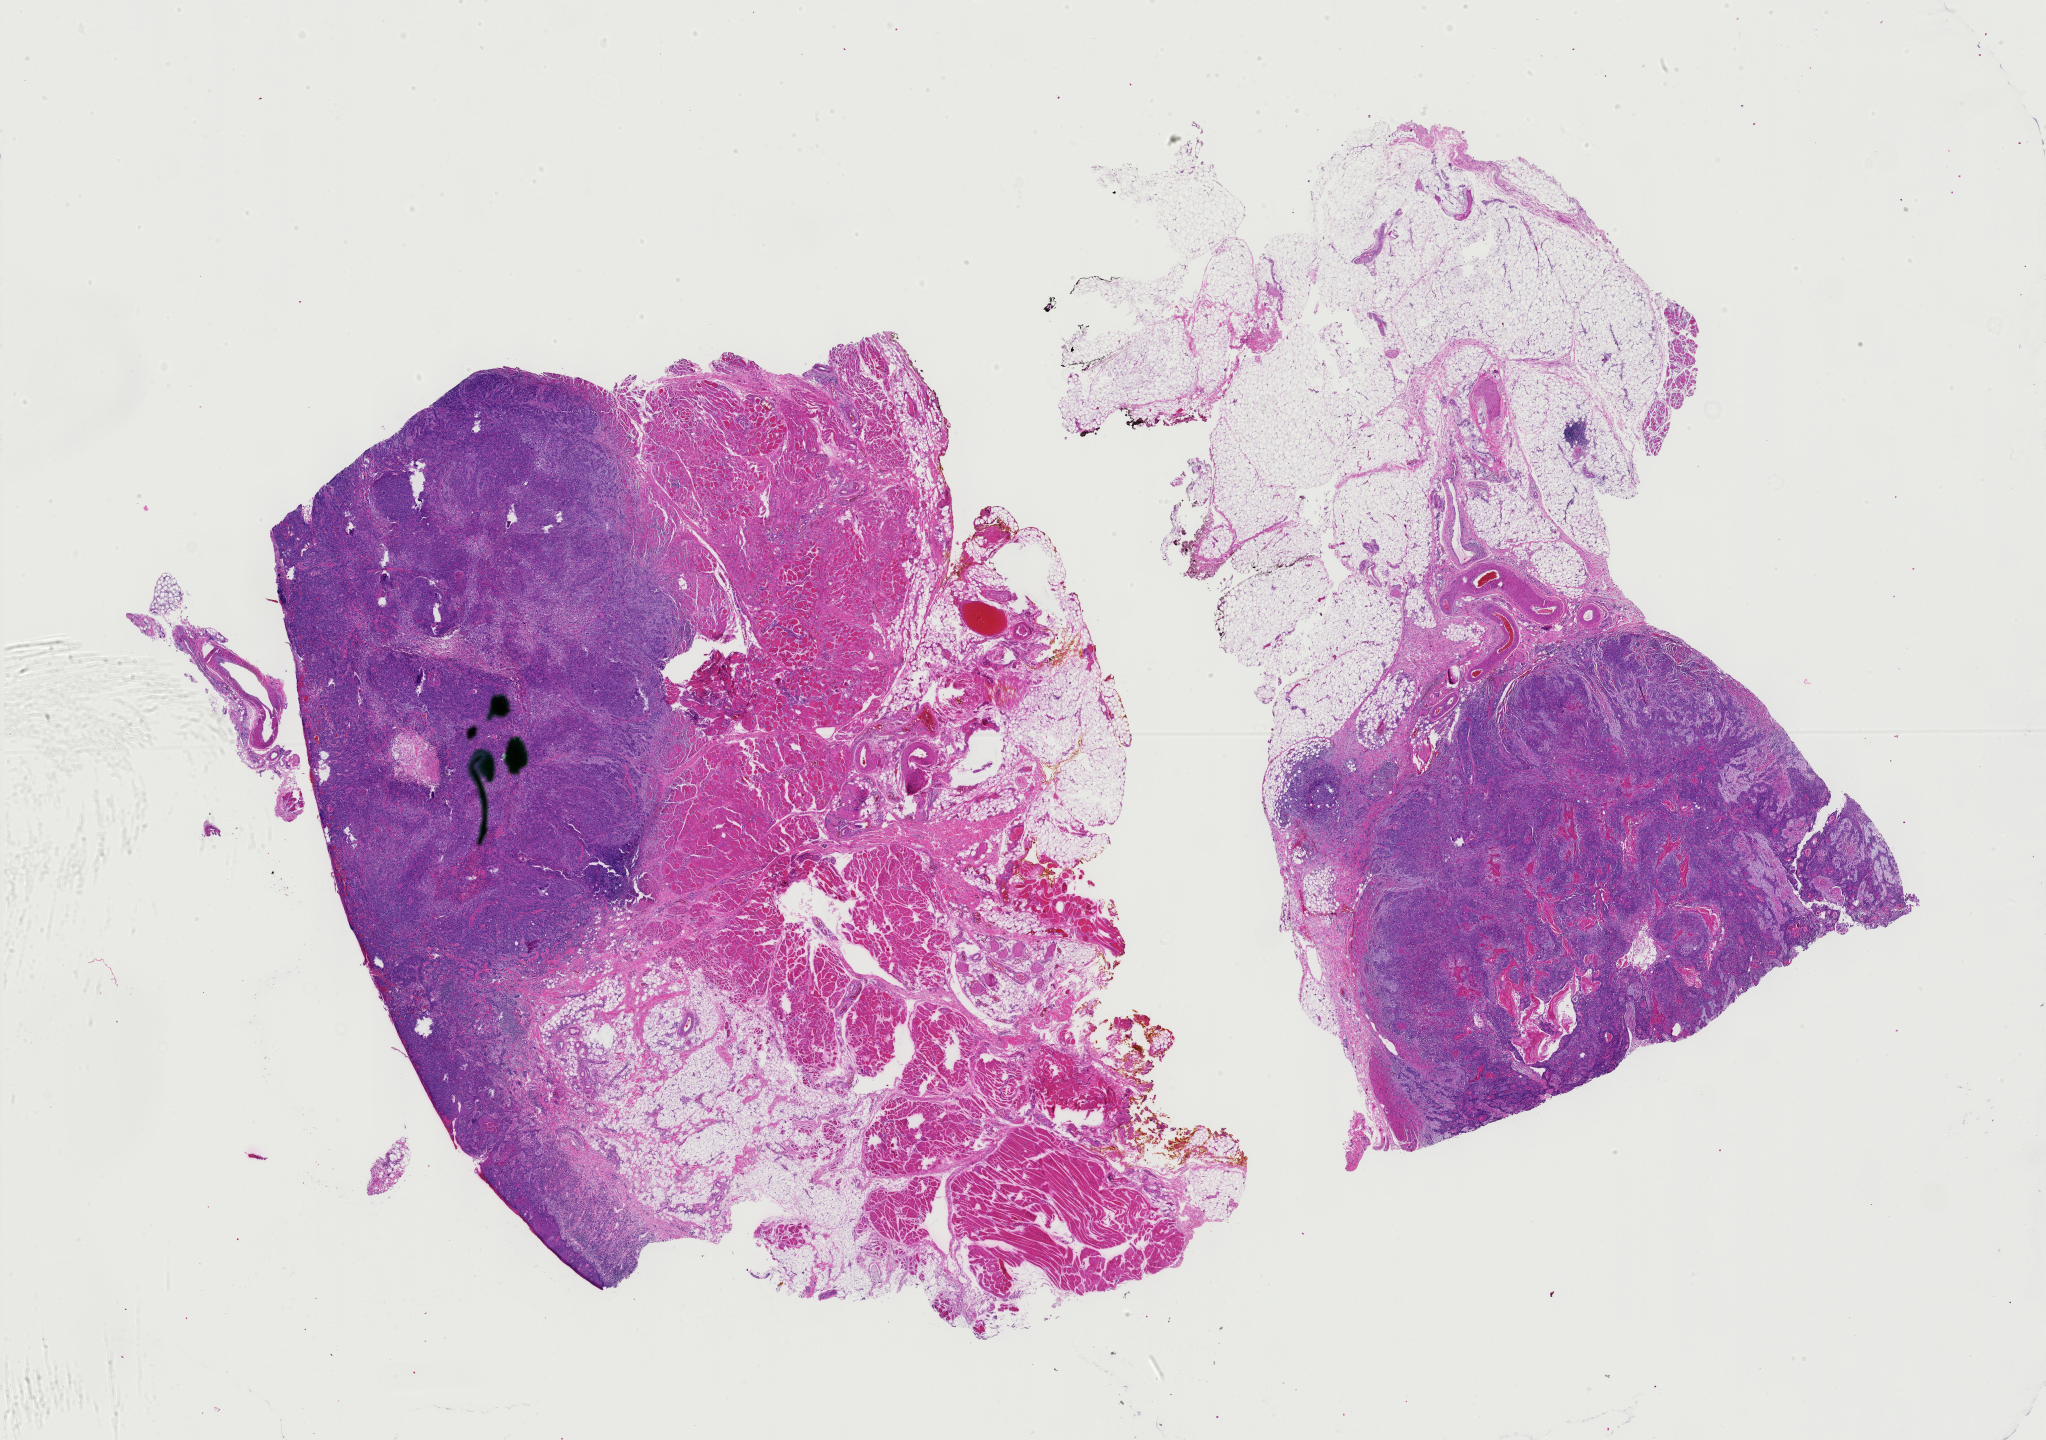
Whole-slide histology image, H&E-stained, whole scanned area (about 29.7 x 20.9 mm, slide scanned at 40x) shown as a low-resolution overview, formalin-fixed paraffin-embedded (FFPE) diagnostic section, primary tumour sample from the head and neck. Male patient; age at initial diagnosis 69 years. Histologic grade: G2 (moderately differentiated).
• pathologic diagnosis: Squamous cell carcinoma, NOS (cheek mucosa)
• TNM: T2 N1 M0
• AJCC pathologic stage: III (7th edition)